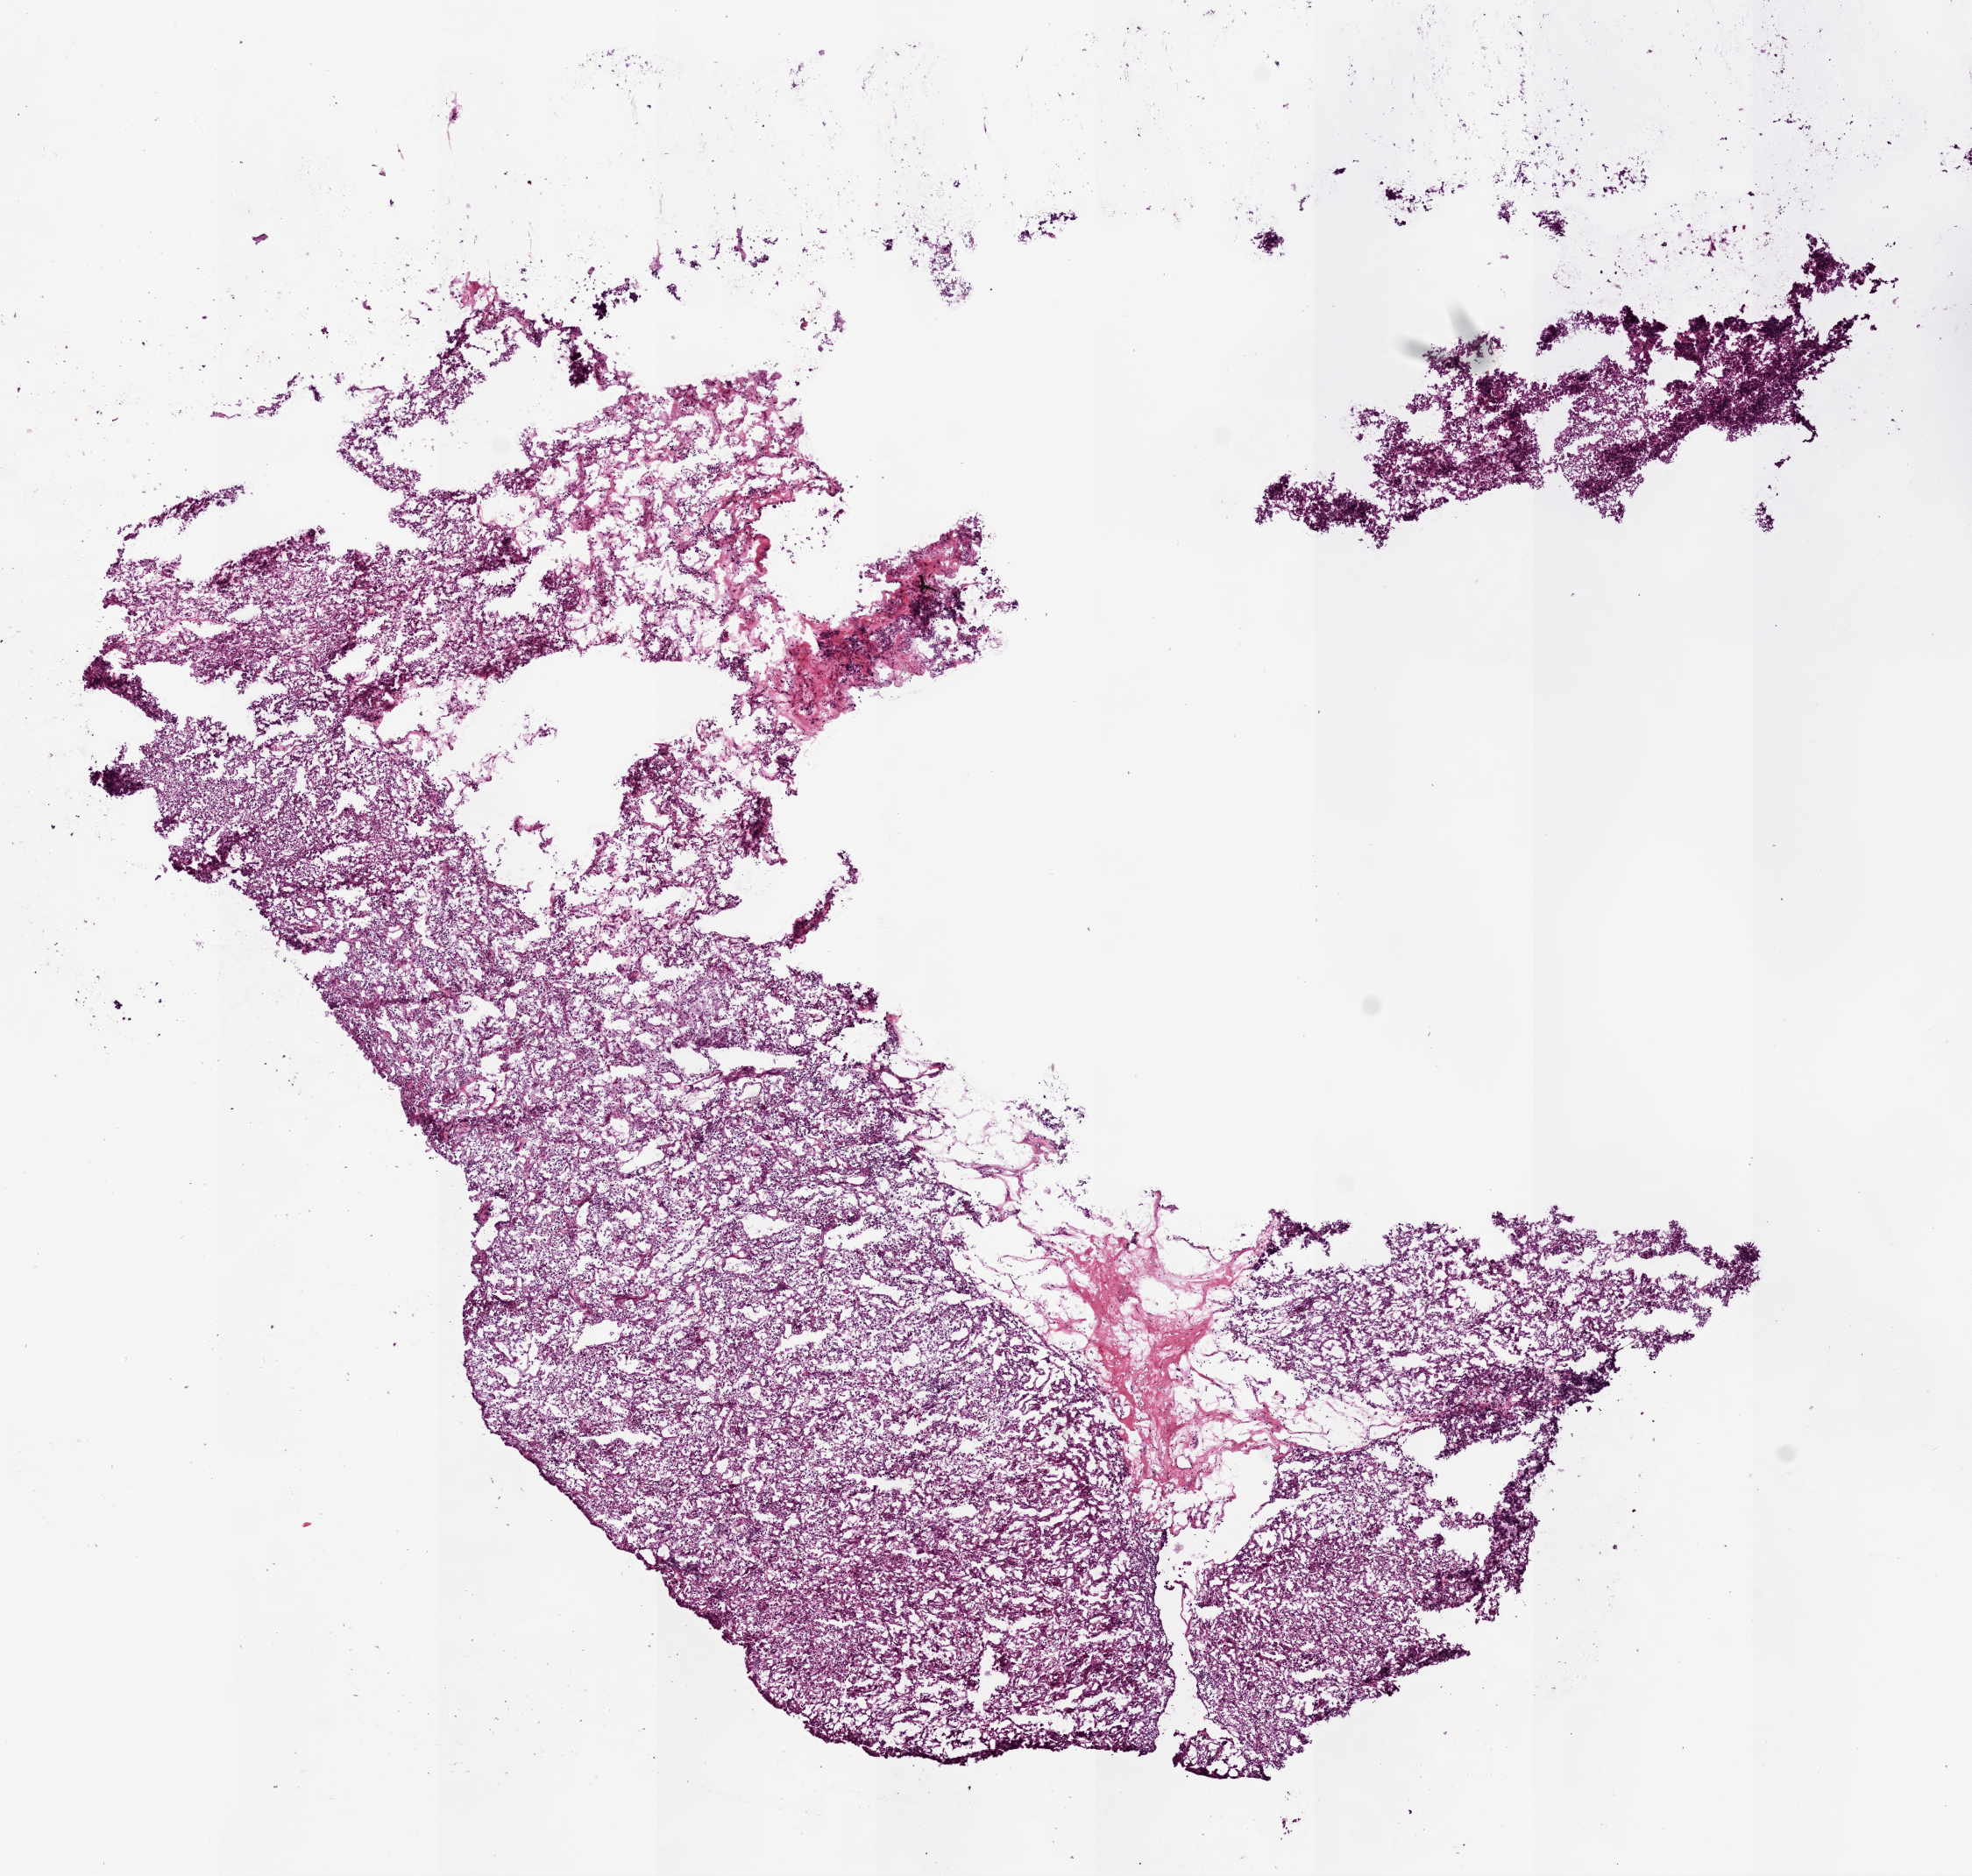
Hematoxylin and eosin (H&E) stained whole-slide image — whole scanned area (about 9.0 x 8.6 mm, from a 20x scan) shown as a low-resolution overview, frozen section, sample: primary tumour, kidney. Patient: male, age at initial diagnosis 55 years. Histologic grade: G2 (moderately differentiated). Pathologist review of this section (percent, as recorded): tumour cells 95%, tumour nuclei 90%, normal cells 0%, stromal cells 5%, necrosis 0%.
TNM: T3b NX M1. Laterality: right. AJCC pathologic stage: IV (6th edition). Diagnosis: Clear cell adenocarcinoma, NOS.